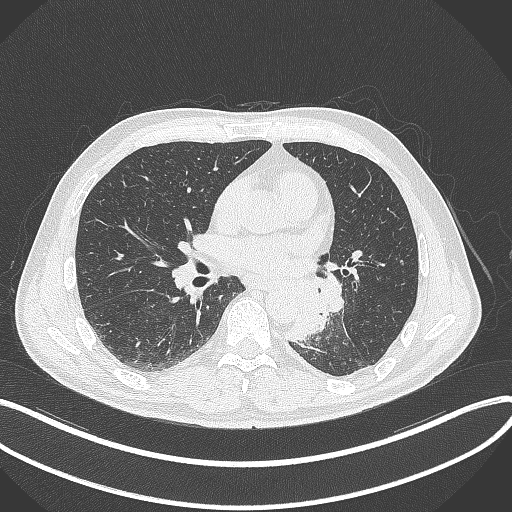
Chest CT, one axial slice; slice 161 of 329 in the series (ordered by position); lung window (W 1500 / L -600 HU); 1 mm slice thickness; 512 × 512 image matrix, field of view 400 × 400 mm. Male patient, age 59 years. From the clinical record (not read from this slice): clinical TNM (as recorded): T2a N2 M0.
Annotated regions visible in this slice (bounding box drawn by a radiologist):
- lung tumour (recorded histology: squamous cell carcinoma): box from (x=288, y=282) to (x=325, y=346) px